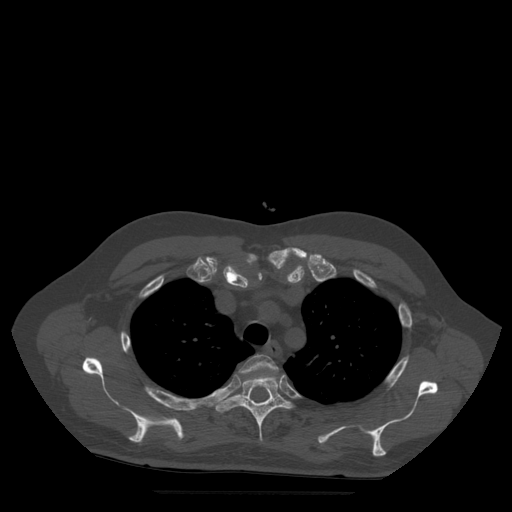
CT including the spine, one axial slice; slice 395 of 522 in the series (ordered by position); bone window (W 1800 / L 400 HU); 1.25 mm slice thickness; 512 × 512 image matrix. Patient age 72 years. From the clinical record (not read from this slice): primary cancer: prostate.
Structures marked on this image (semi-automatic segmentation, software-assisted and operator-edited):
- T3 vertebra: bounding box <239,355,278,374> (left, top, right, bottom; pixels)
- T4 vertebra: <216,374,293,442>